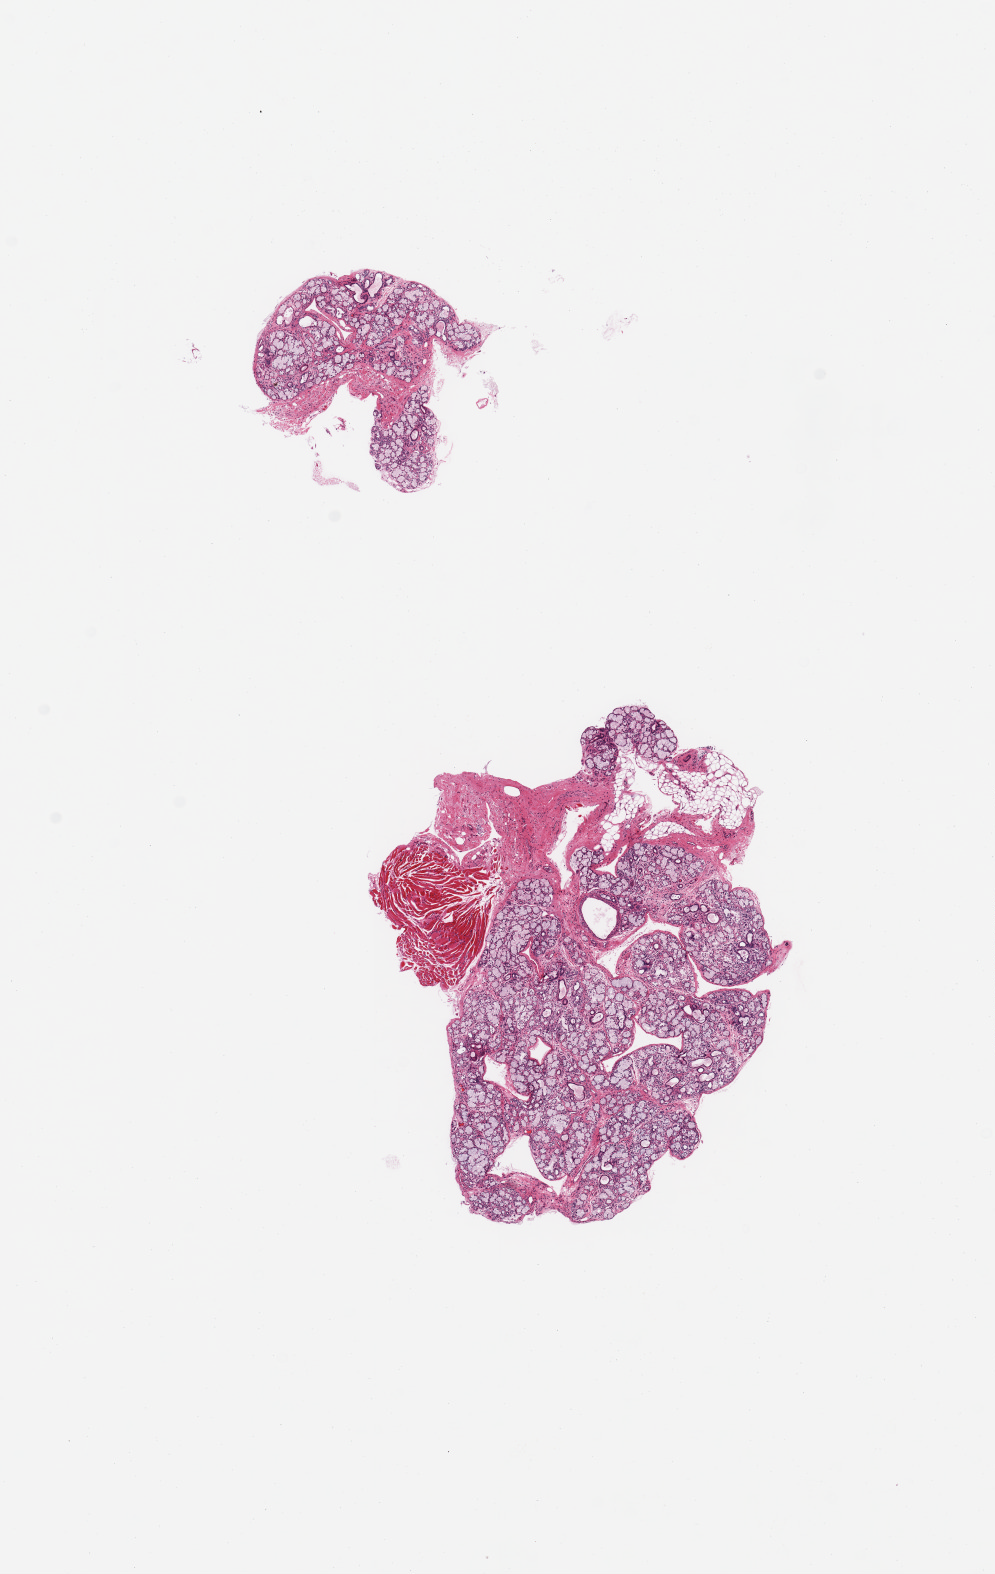
Hematoxylin and eosin (H&E) whole-slide image, brightfield — shown as a low-resolution overview of the whole scanned area (about 7.9 x 12.5 mm, from a 20x scan); PAXgene-fixed paraffin-embedded (PFPE) section; target tissue: minor salivary gland; donor tissue sample.
Pathologist's review note for this sample: 2 pieces, ~80% glandular elements.